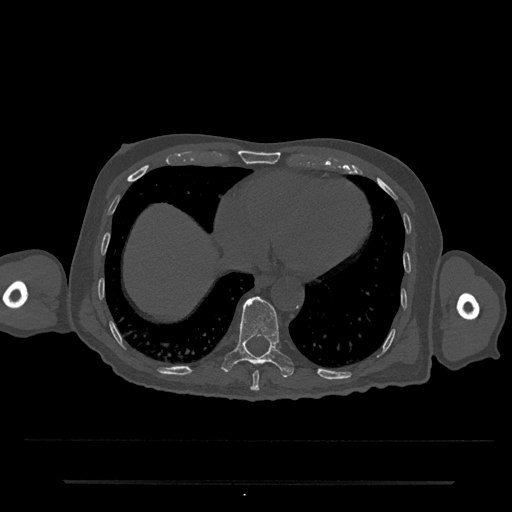
CT including the spine, one axial slice. Position 321 of 797 along the scan axis. 120 kVp. Bone window (W 1800 / L 400 HU). 0.5 mm slice thickness. 512 × 512 image matrix. Male patient, age 74 years. From the clinical record (not read from this slice): primary cancer: prostate.
Outlined on this slice (semi-automatically segmented with operator editing):
- T10 vertebra: bounding box [x1, y1, x2, y2] px = [222, 296, 294, 378]
- T9 vertebra: [250, 370, 259, 391]